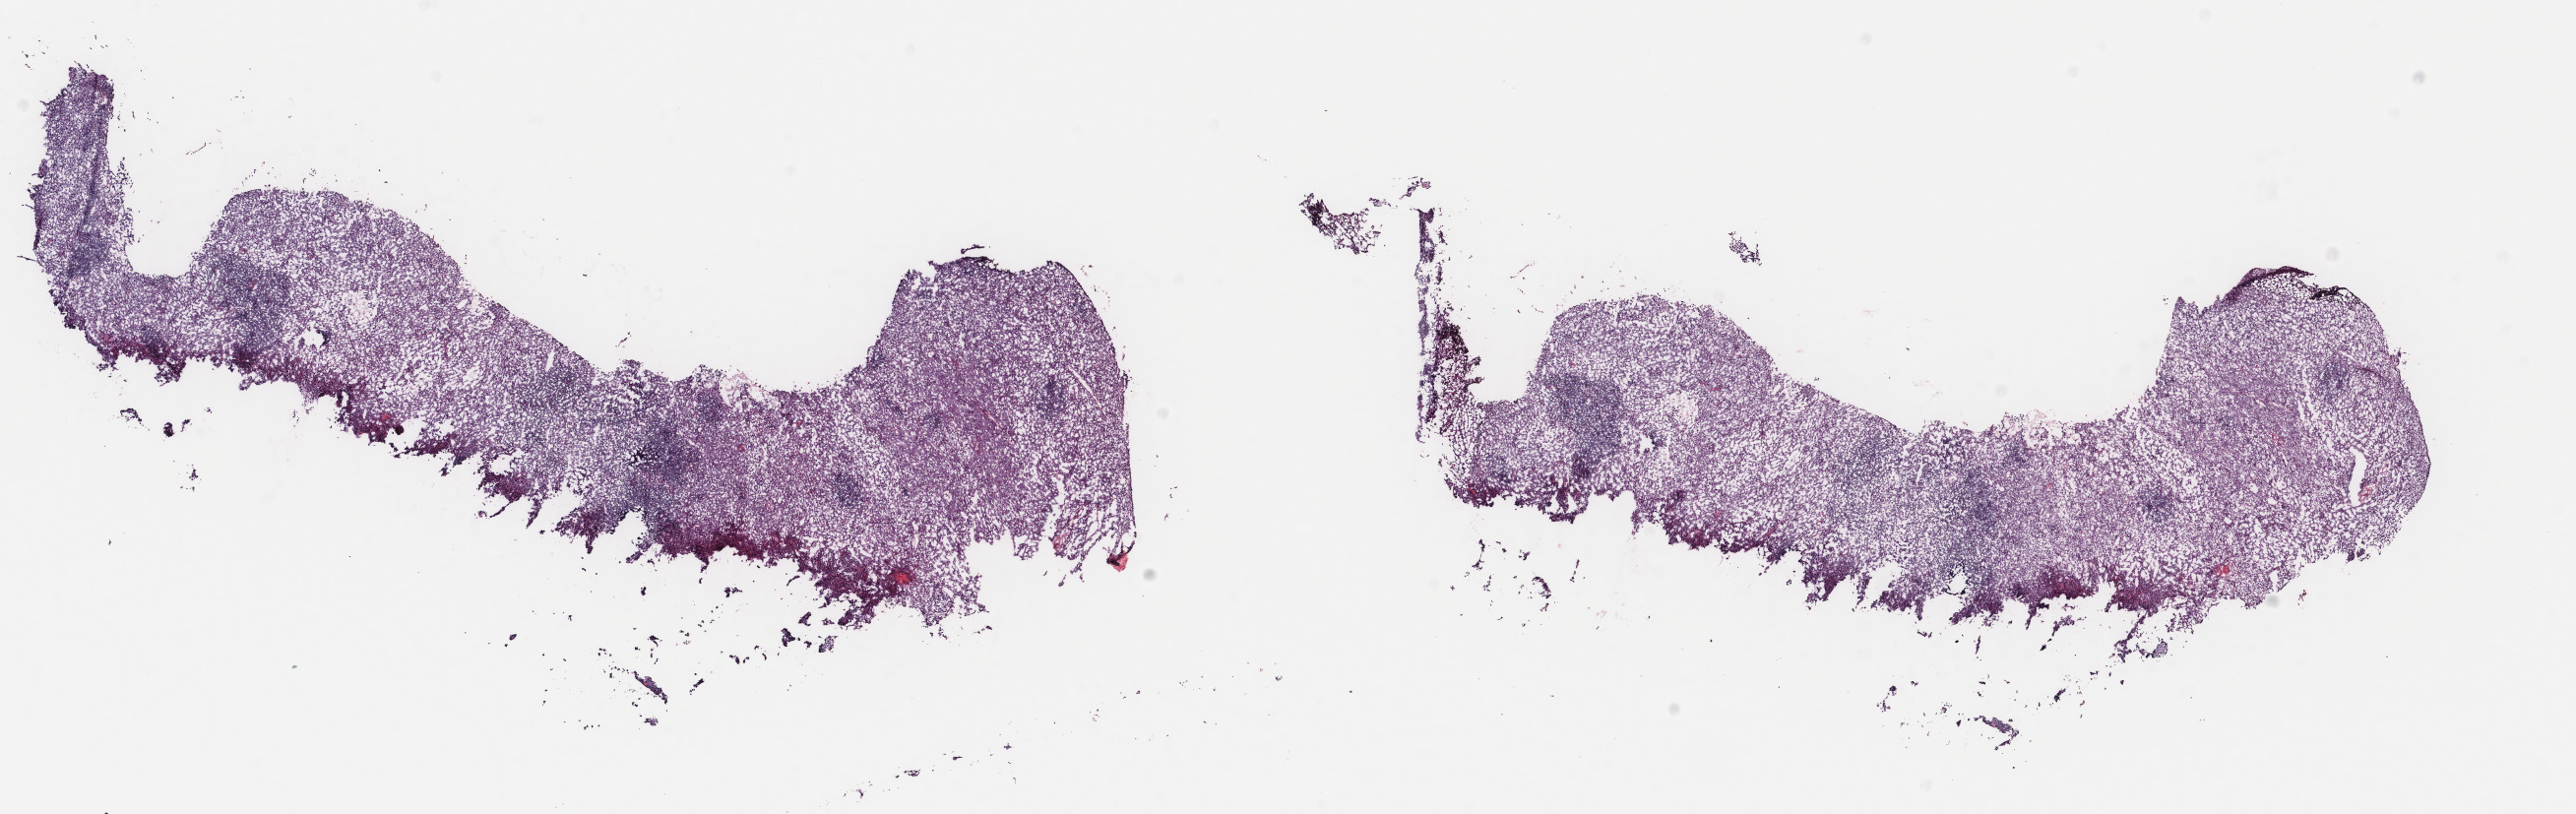
Digitized H&E-stained tissue section (whole slide) — shown as a low-resolution overview of the whole scanned area (about 20.8 x 6.6 mm, acquisition: 40x scan), frozen section, metastatic tumour sample, sampled site not recorded. Male, age 66 years at initial diagnosis. Pathologist review of this section (percent, as recorded): tumour cells 100%, tumour nuclei 90%, normal cells 0%, stromal cells 0%, necrosis 0%. Infiltration values recorded for this section: lymphocyte infiltration 0%, monocyte infiltration 0%, neutrophil infiltration 0%.
• this section: metastatic tumour tissue
• patient diagnosis: Malignant melanoma, NOS